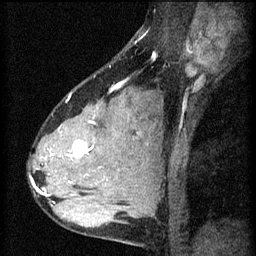
Breast MRI (dynamic contrast-enhanced), one sagittal slice; 3 images stored at this slice position (order not interpretable as contrast timing); 1.5 T; TE 4.2 ms, TR 8.2 ms; 2 mm slice thickness; 256 × 256 image matrix. Patient: female, 37 years.
Structures marked on this image (semi-automatically segmented with operator editing):
- analysis volume of interest (the breast-tissue region the enhancement analysis was run in; not a lesion): bounding box (x1, y1, x2, y2) in pixels: (44, 102, 119, 197)
- tumour enhancement mask (voxels above the 70 % enhancement threshold inside the analysis volume of interest): (67, 112, 96, 159)